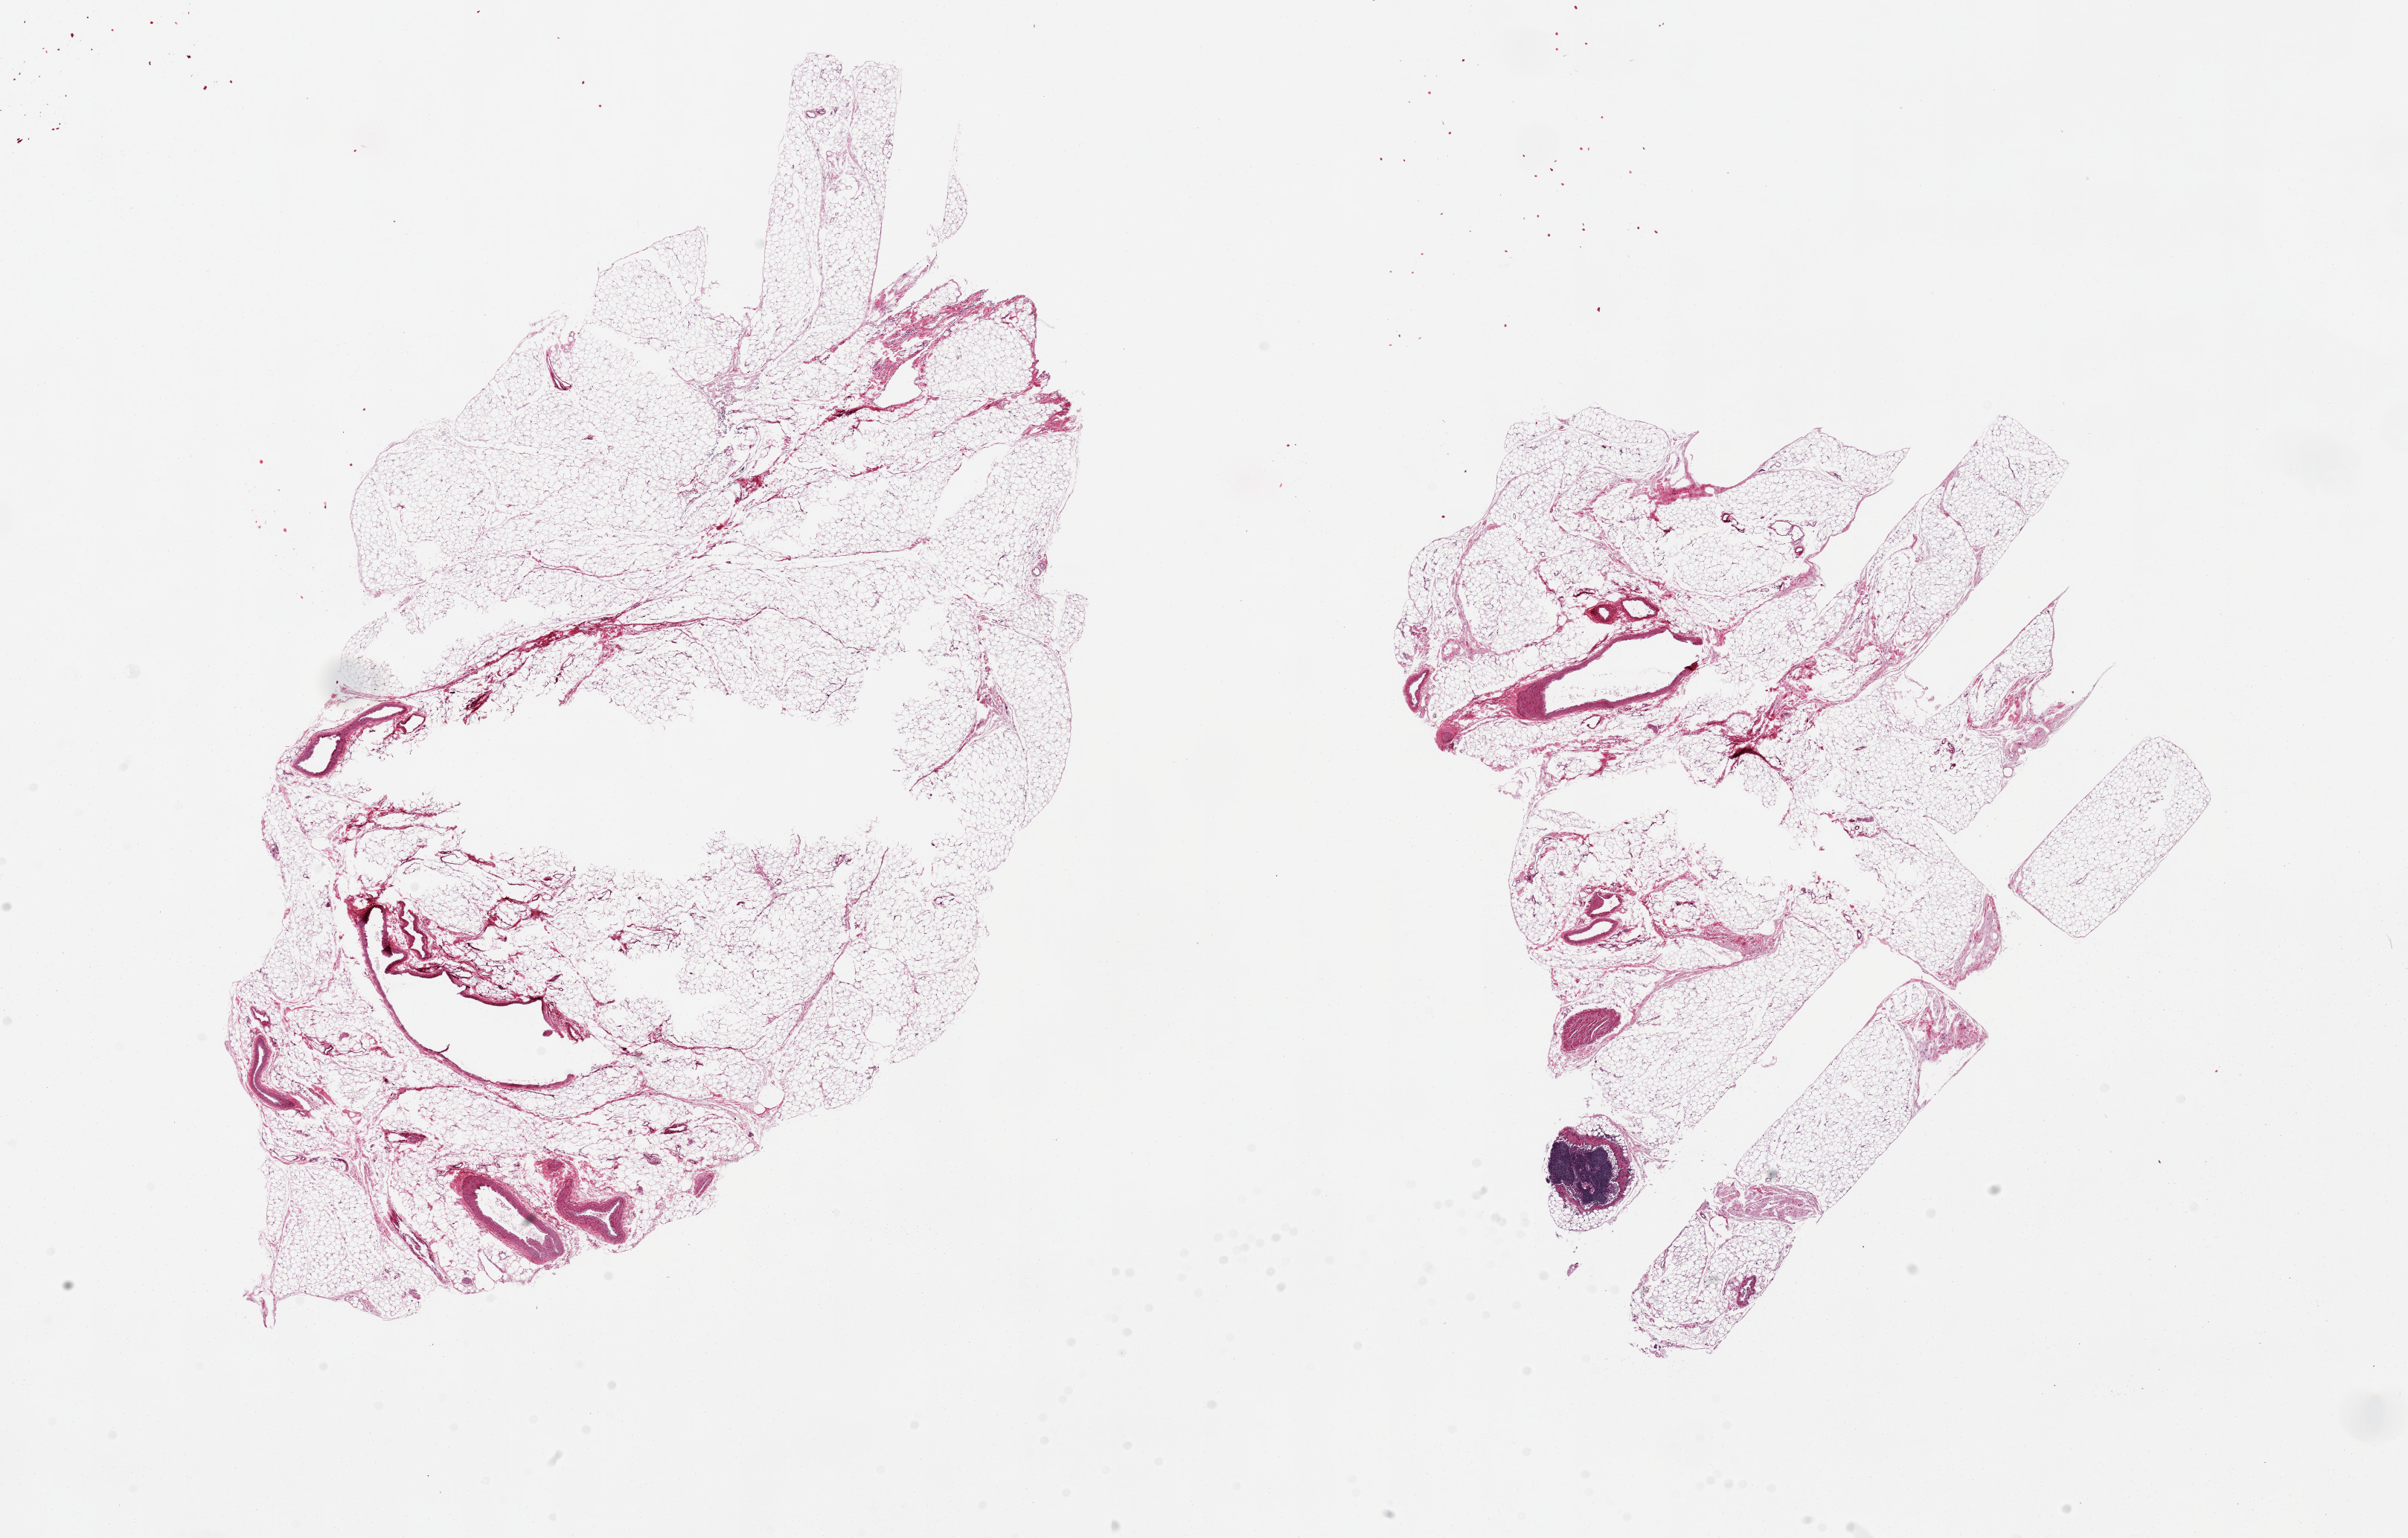
Whole-slide image, hematoxylin and eosin (H&E) stain — shown as a low-resolution overview of the whole scanned area (about 25.6 x 16.3 mm, slide scanned at 20x). PAXgene-fixed, paraffin-embedded tissue. Target tissue: omentum. Donor tissue sample. Donor sex: female.
Reviewer comment on this tissue sample: 2 pieces; 15x9 & 10x10mm; 1 with 1mm lymph nodule; Central holes.